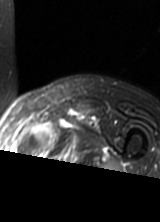
MRI of an extremity soft-tissue mass, one axial slice; slice 52 of 69 in the series (ordered by position); T2-weighted fat-saturated; MR volume resampled by the dataset authors to the PET/CT grid (not the native acquisition matrix); 160 × 222 image matrix. Female patient. From the clinical record (not read from this slice): histological type: pleomorphic leiomyosarcoma; grade: high; site of the primary tumour: left thigh.
Structures marked on this image (expert contour drawn on MRI and transferred to this co-registered scan by the dataset authors):
- gross tumour volume including surrounding oedema: bounding box <25,125,76,153> (left, top, right, bottom; pixels)